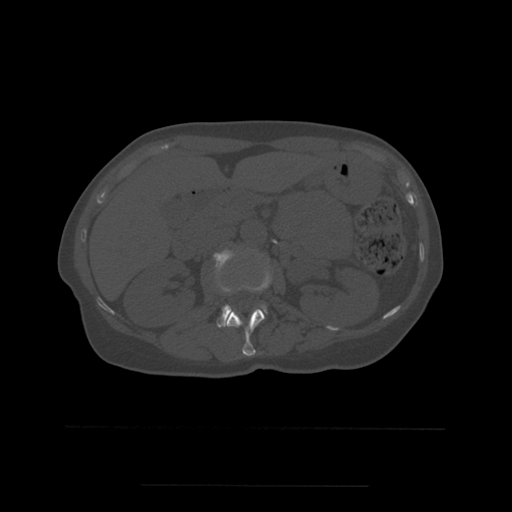
CT including the spine, one axial slice. Slice 225 of 544 in the series (ordered by position). Bone window (W 1800 / L 400 HU). 1.25 mm slice thickness. 512 × 512 image matrix. Patient age 58 years. Case-level facts recorded for this patient, not image findings: primary cancer: lung.
Annotated regions visible in this slice (semi-automatic segmentation, software-assisted and operator-edited):
- L1 vertebra: bounding box <226,267,272,357> (left, top, right, bottom; pixels)
- L2 vertebra: <215,251,267,328>